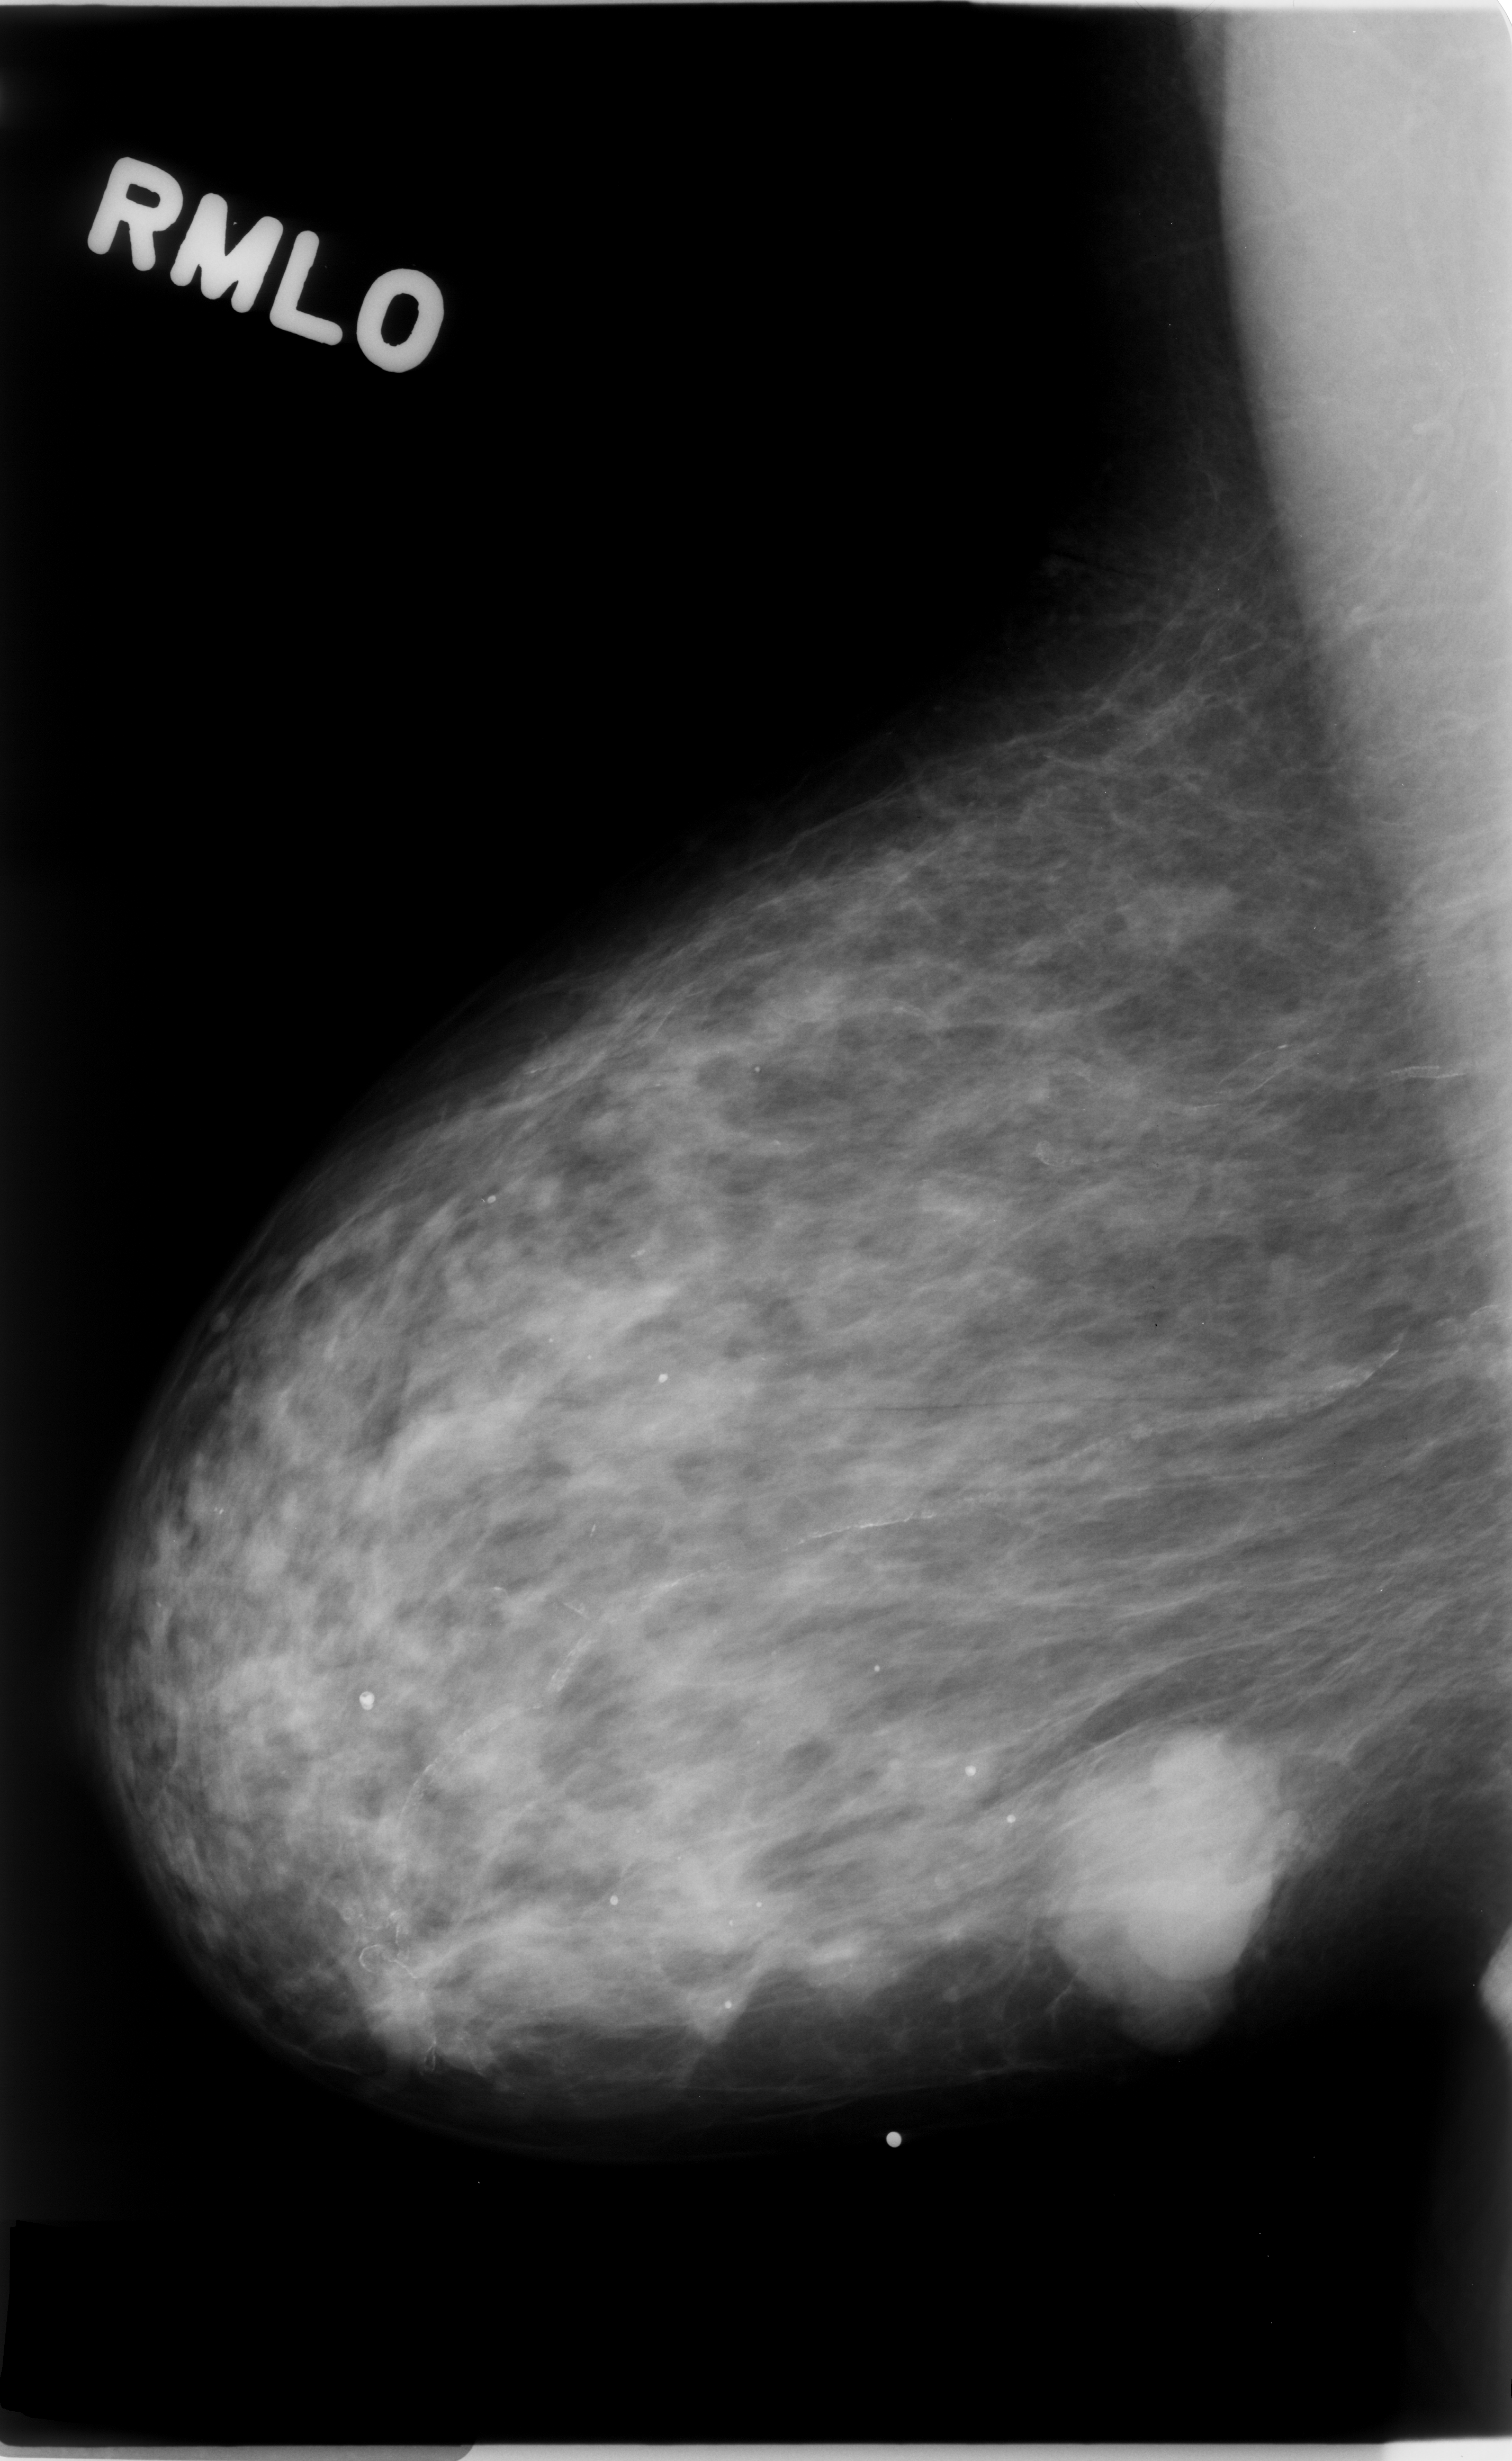
Mammogram (digitized film). Right breast. MLO view. 1512 × 2461 image matrix.
Marked abnormalities (boxes around the expert regions of interest):
- mass, shape lobulated, margins microlobulated; BI-RADS assessment category 5; subtlety rating 5 on a 1 (subtle) to 5 (obvious) scale; pathology result (as recorded, not read from the image): malignant: bounding box (x1, y1, x2, y2) in pixels: (1045, 1774, 1246, 1992)